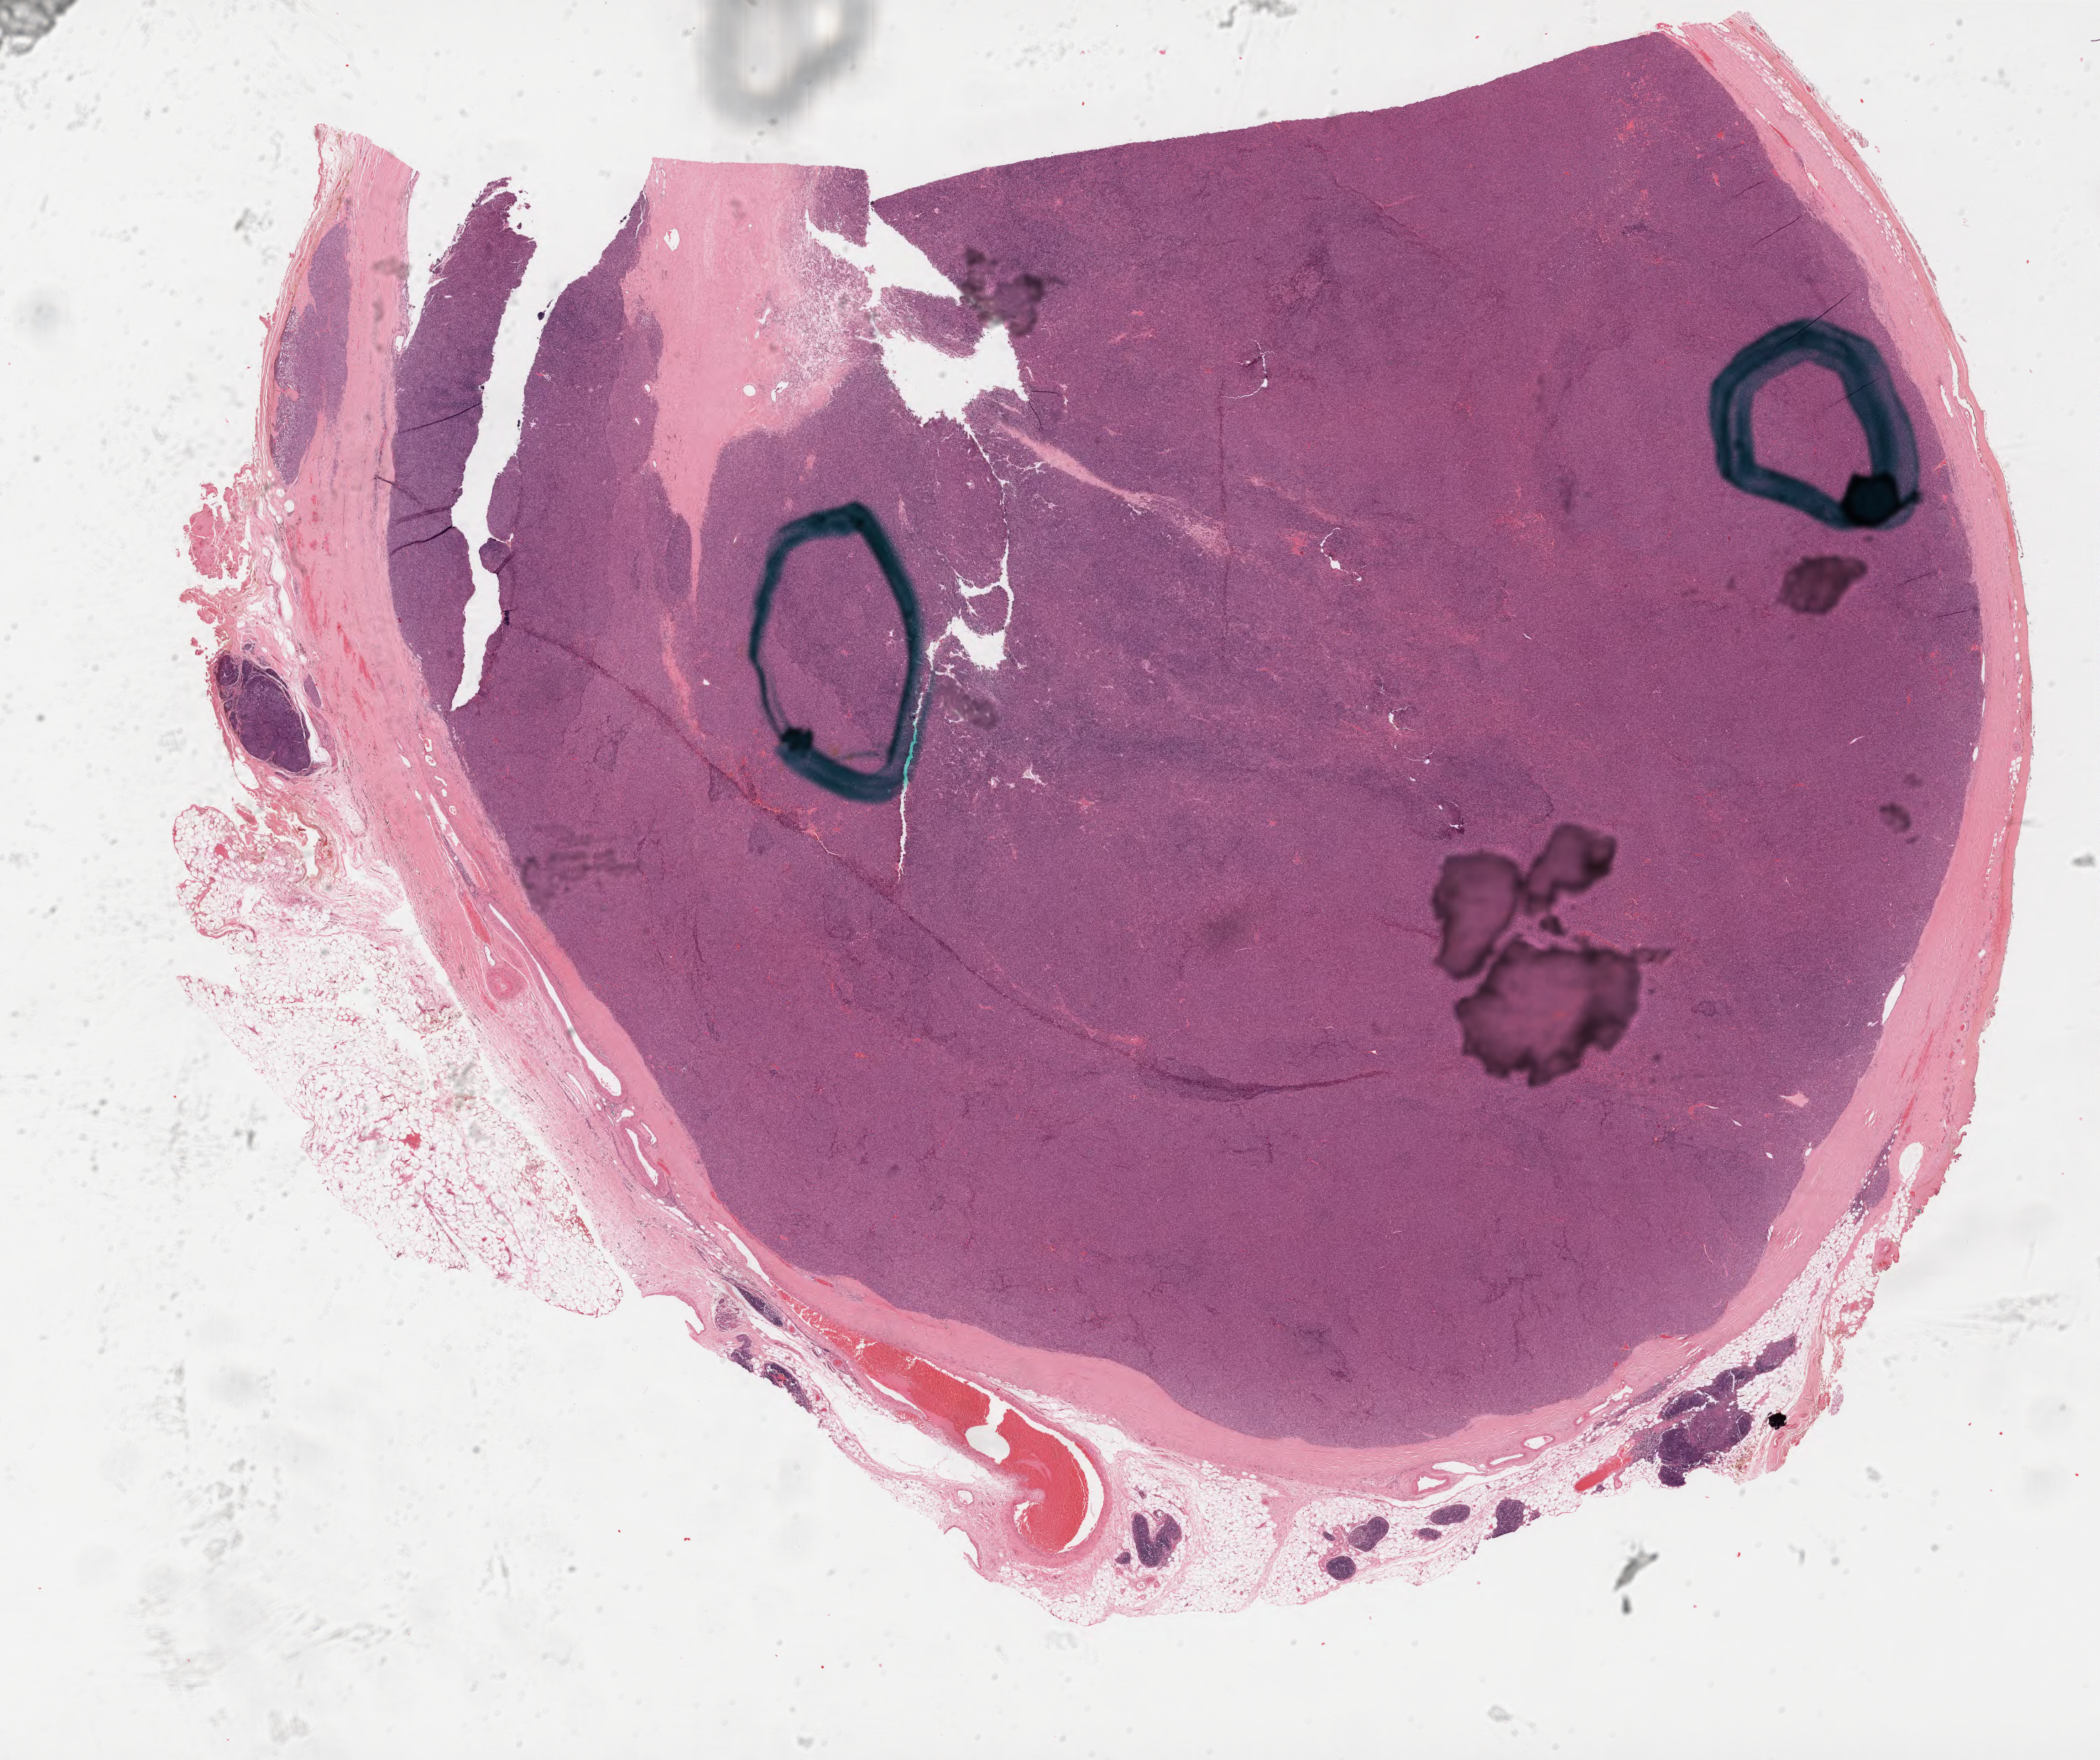
Whole-slide histology image, H&E-stained — shown as a low-resolution overview of the whole scanned area (about 23.8 x 19.9 mm), formalin-fixed paraffin-embedded (FFPE) diagnostic section, primary tumour sample from the thymus. Patient: female, age at initial diagnosis 76 years.
Diagnosis: Thymoma, type AB, malignant.